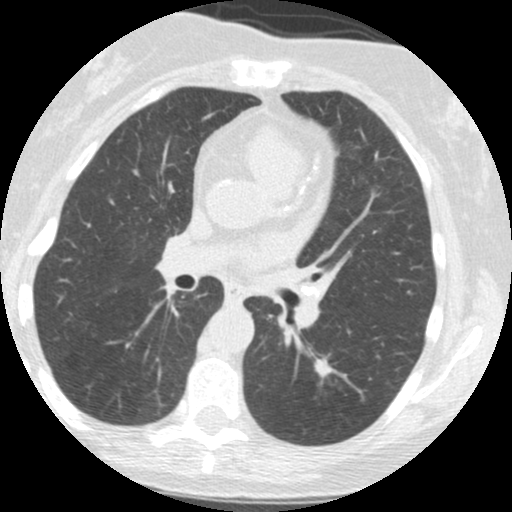
Low-dose screening chest CT, axial slice. Baseline annual screen. Lung window (W 1500 / L -600 HU). 2.5 mm slice thickness. Slice 67 of 147 in the series. Female participant, aged 61 years at enrolment. Current smoker at enrolment.
• Lesion marked by an expert reader, box from (x=302, y=341) to (x=350, y=393) px.
• Reader record for this screening exam (exam-level; its link to the box is not recorded): non-calcified nodule or mass ≥4 mm, left lower lobe, 12 × 11 mm, spiculated (stellate) margins, soft tissue attenuation.
• Later outcome: lung cancer diagnosed 440 days after this screen — squamous cell carcinoma, NOS, left lower lobe, moderately differentiated (G2), stage IA (AJCC 6th edition), 12 mm at pathology.